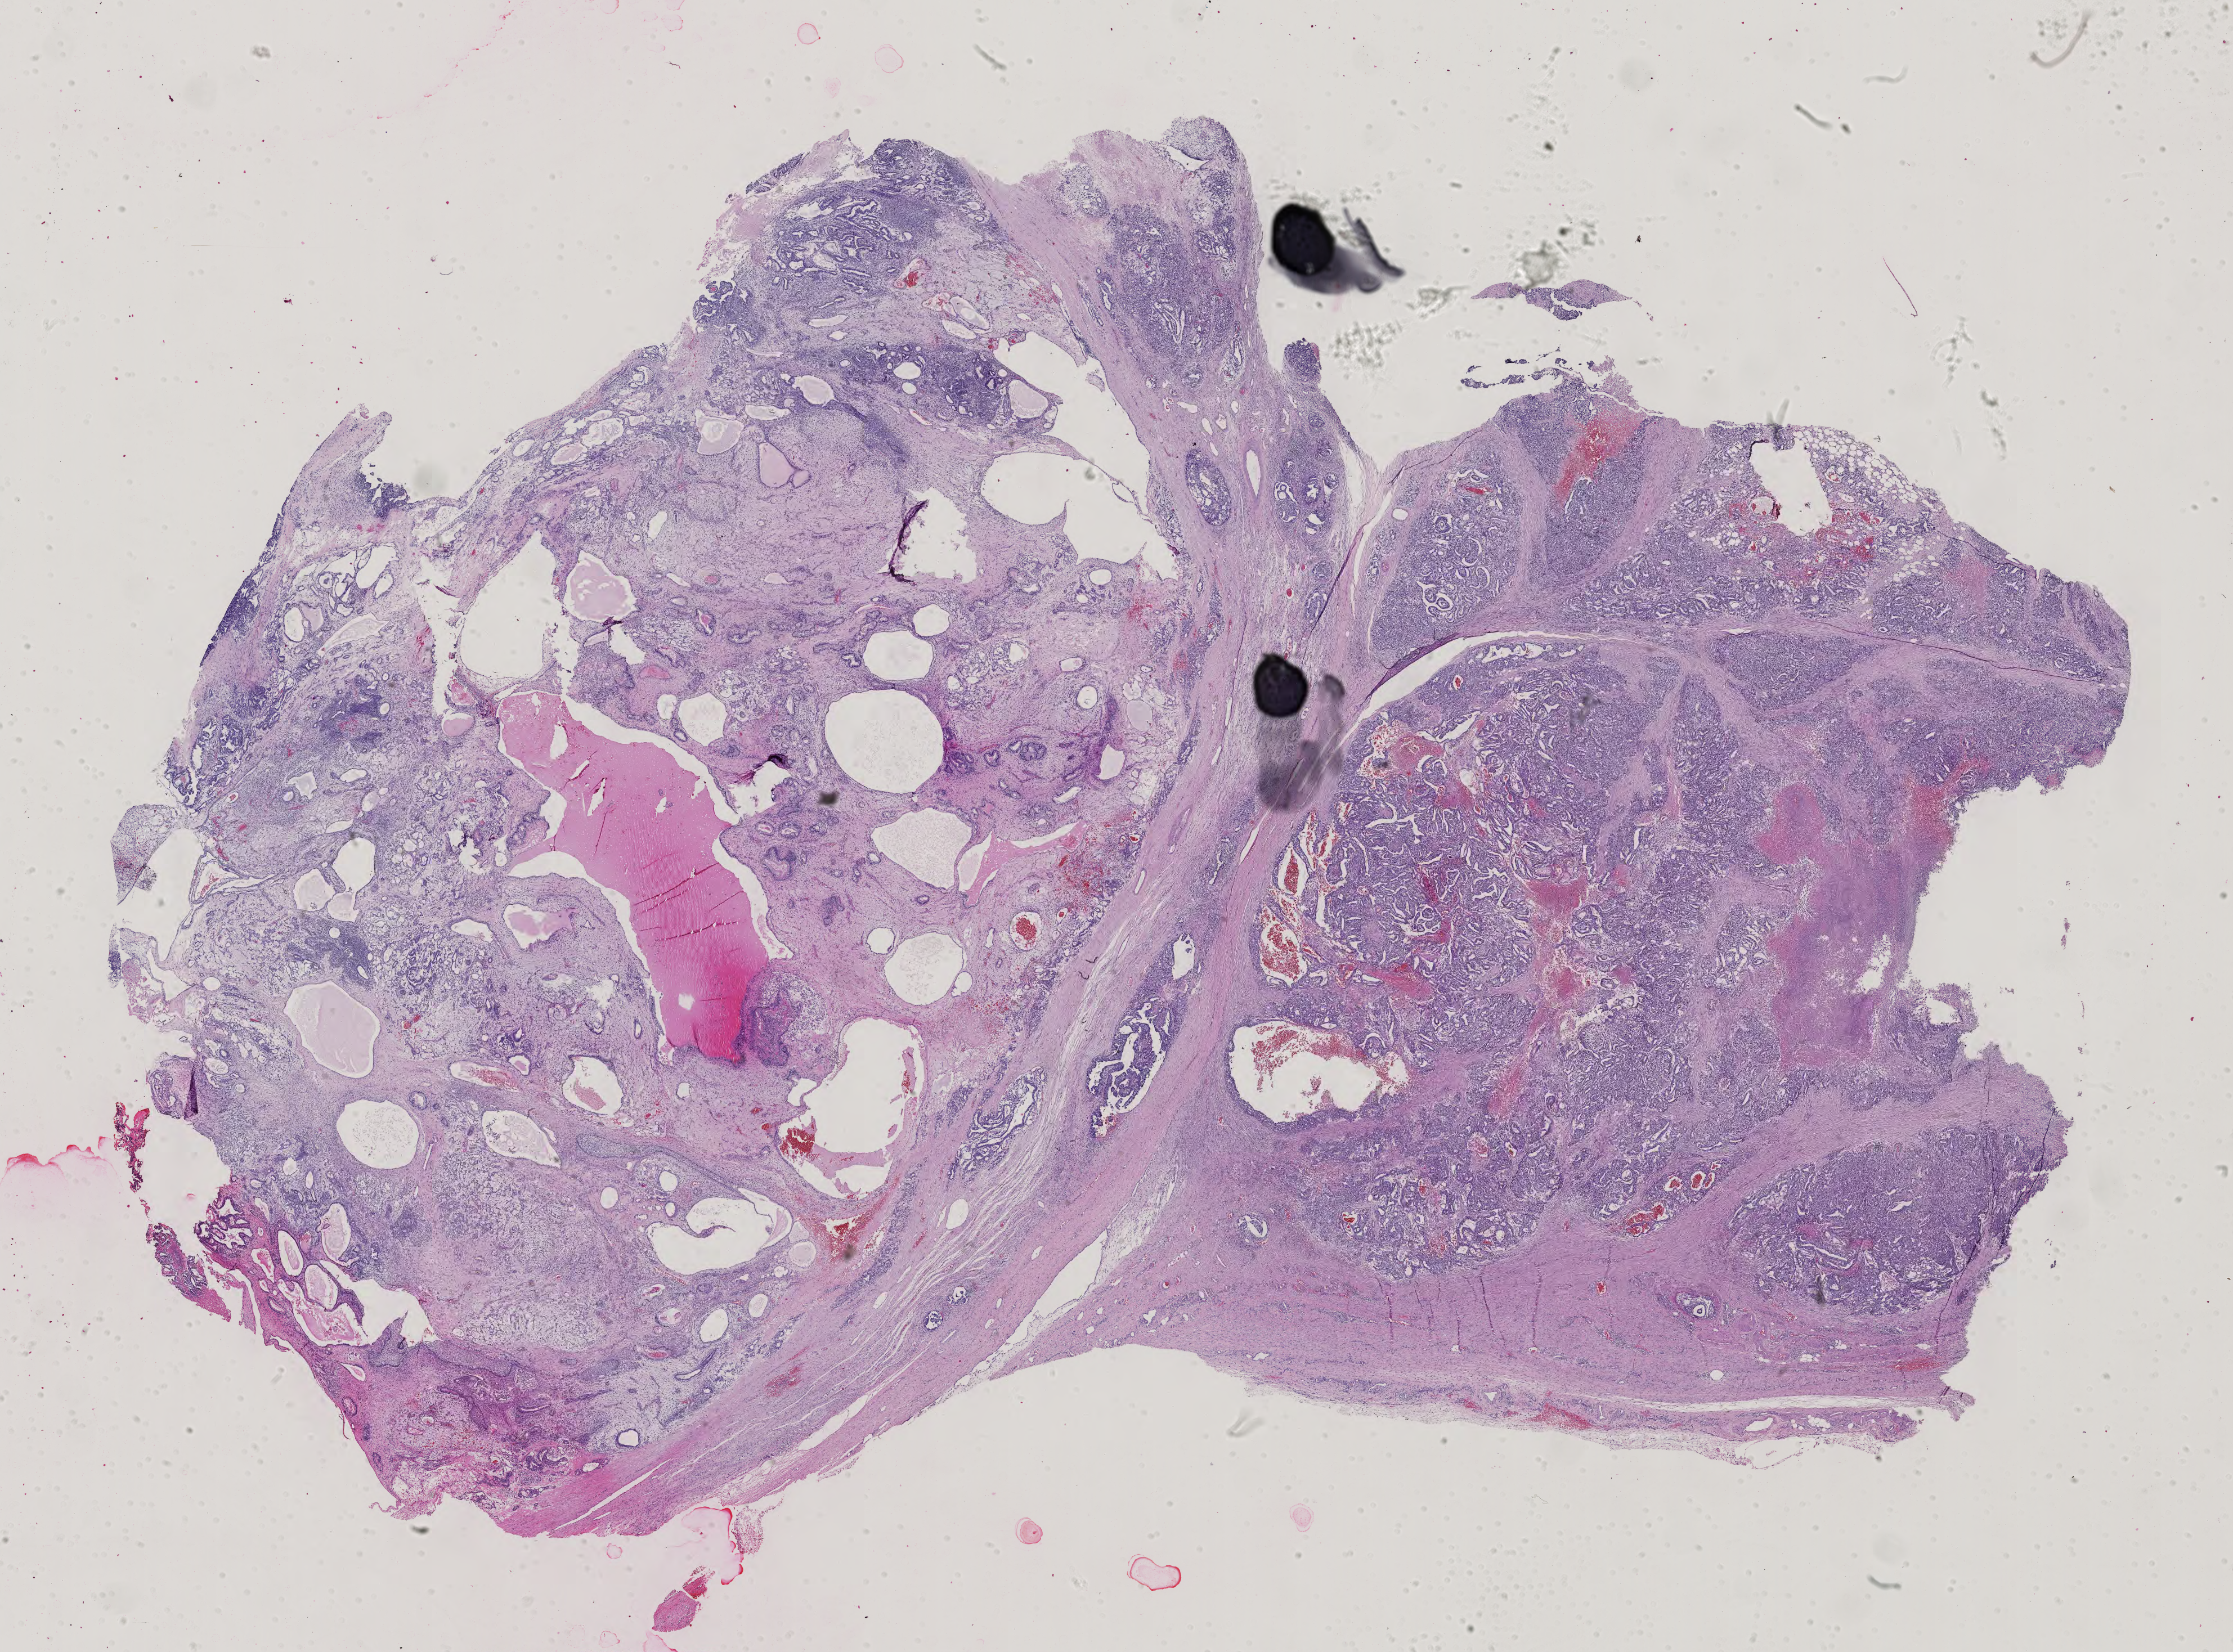
Digitized H&E tissue section (whole slide) — low-resolution overview of the scanned area, about 28.9 x 21.4 mm (from a 40x scan), formalin-fixed paraffin-embedded (FFPE) diagnostic section, primary tumour sample from the testis. Patient: male, age at initial diagnosis 32 years.
AJCC pathologic stage: III. Laterality: right. Pathologic diagnosis: Mixed germ cell tumor.